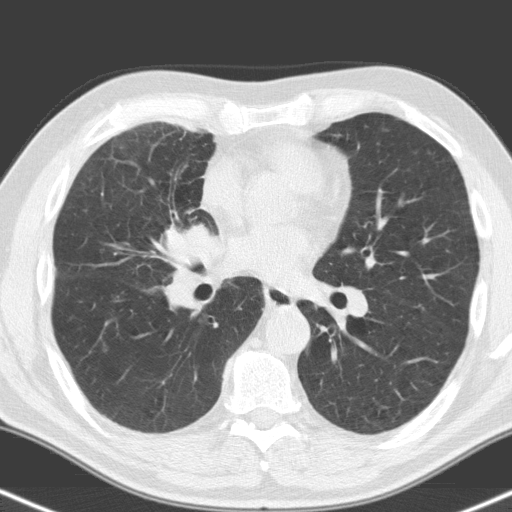
Low-dose screening chest CT, one axial slice. Lung window (W 1500 / L -600 HU). 3.2 mm slice thickness. 512 × 512 image matrix, field of view 324 × 324 mm.
Annotated regions visible in this slice (manually delineated by an expert):
- lesion 1 (tumor, hilum of right lung): bounding box [x1, y1, x2, y2] px = [167, 226, 224, 308]